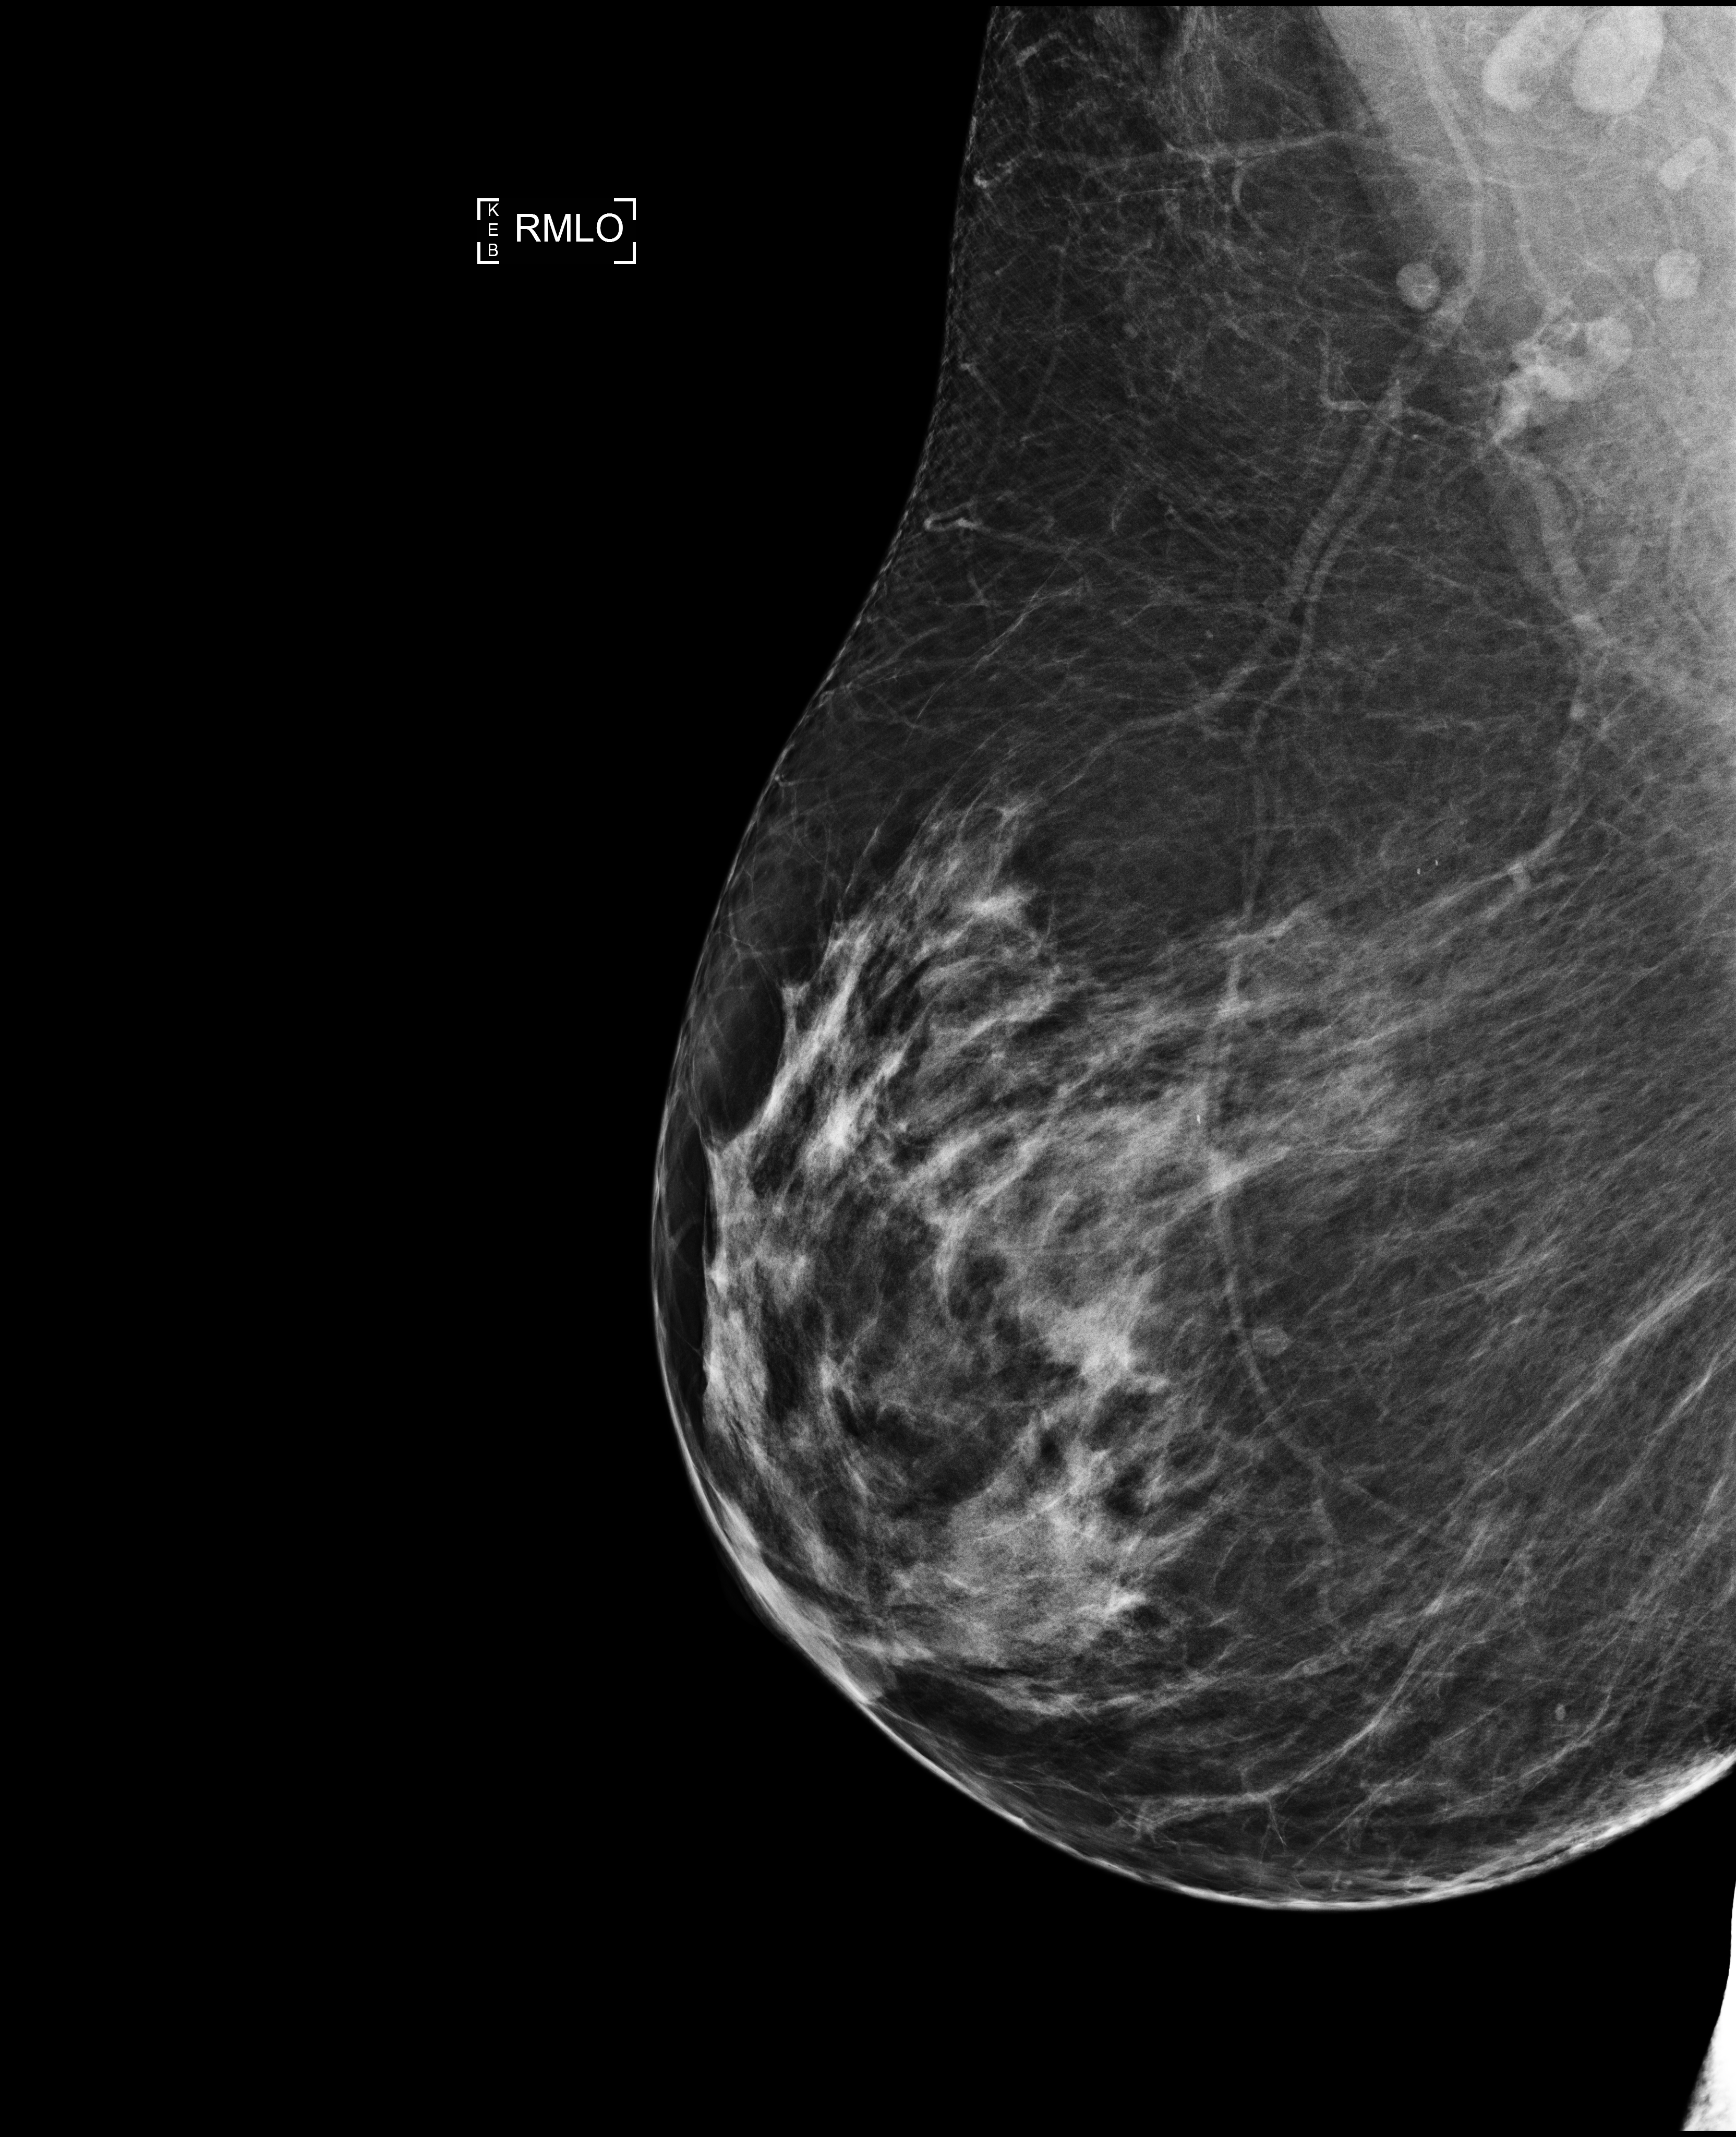
Digital mammogram (FFDM); right breast; mediolateral oblique (MLO) view; annual screening mammography examination; compressed breast thickness 85 mm. Patient aged 64 years (female).
Final BI-RADS category for the screening round (tomosynthesis exam, both breasts): category 1.